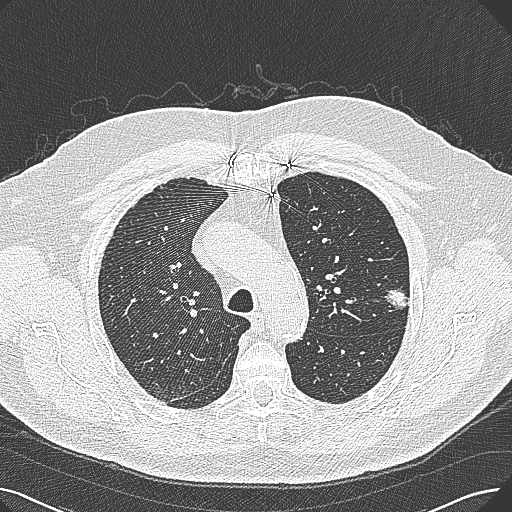
Chest CT (low-dose screening protocol), one axial image, baseline annual screen, lung window (W 1500 / L -600 HU), slice 77 of 269 in the series. Male, age 74 years at enrolment. Former smoker at enrolment.
Expert-annotated lung lesion, box from (x=375, y=273) to (x=424, y=318) px. Reader record for this screening exam (exam-level; its link to the box is not recorded): non-calcified nodule or mass ≥4 mm, left upper lobe, 15 × 10 mm, poorly defined margins, soft tissue attenuation.